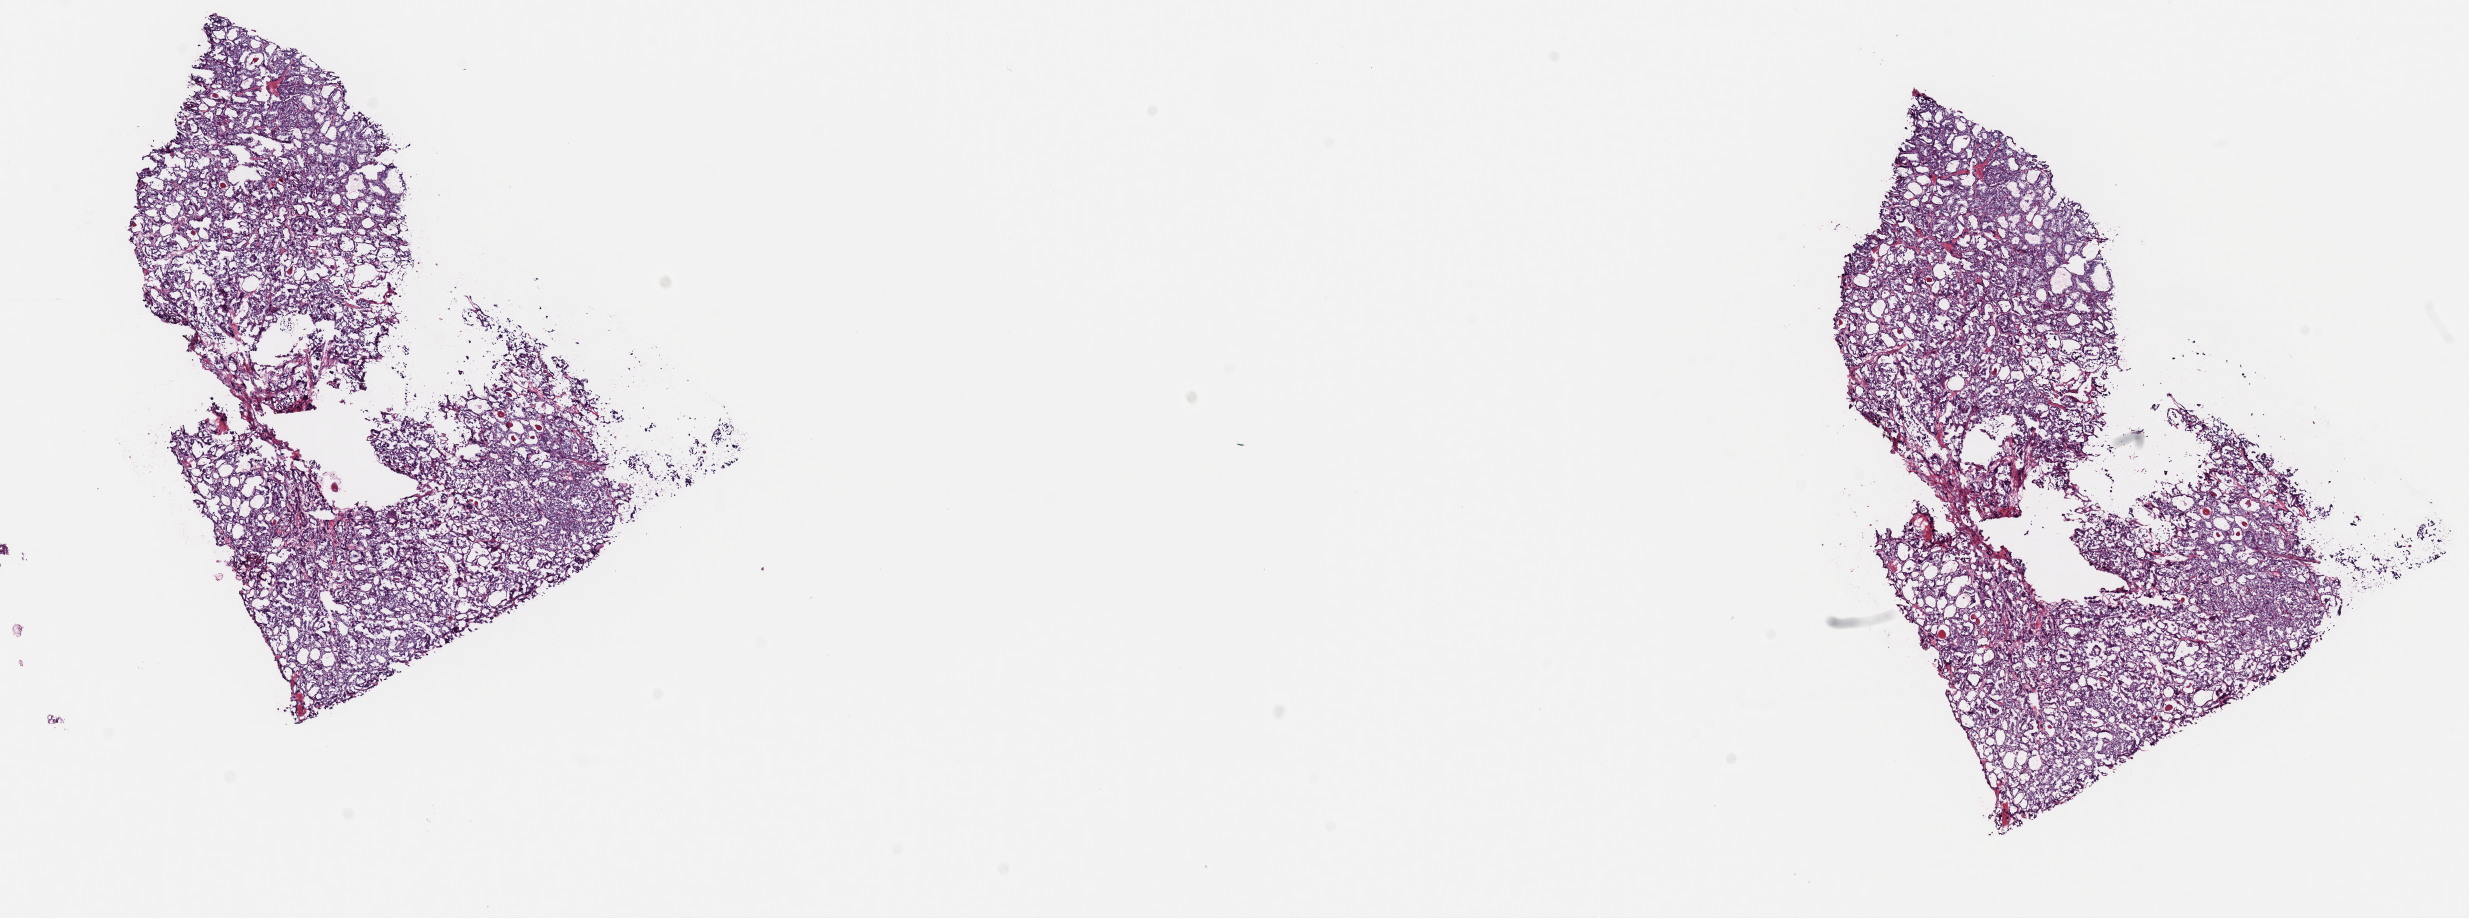
Digitized H&E-stained tissue section (whole slide), a low-resolution overview of the entire scanned area, about 19.5 x 7.3 mm (slide scanned at 40x), frozen section from the top of the tissue portion, sample: primary tumour, thyroid. Patient: female, age at initial diagnosis 47 years. Pathologist review of this section (percent, as recorded): tumour cells 80%, tumour nuclei 88%, normal cells 5%, stromal cells 15%, necrosis 0%. Infiltration values recorded for this section: lymphocyte infiltration 0%, monocyte infiltration 0%, neutrophil infiltration 0%.
- AJCC pathologic stage: III (7th edition)
- histologic diagnosis: Papillary adenocarcinoma, NOS (thyroid gland)
- TNM: T2 N1a MX